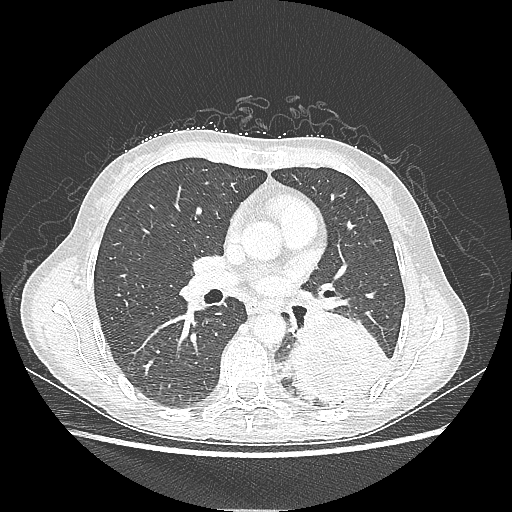
Chest CT, one axial slice; slice 119 of 220 in the series (ordered by position); reconstruction kernel LUNG; 80 kVp; lung window (W 1500 / L -600 HU); 1.25 mm slice thickness; 512 × 512 image matrix. Patient: female, 53 years. From the clinical record (not read from this slice): clinical TNM (as recorded): T3 N0 M0.
Structures marked on this image (bounding box drawn by a radiologist):
- lung tumour (recorded histology: adenocarcinoma): bounding box <290,311,390,405> (left, top, right, bottom; pixels)